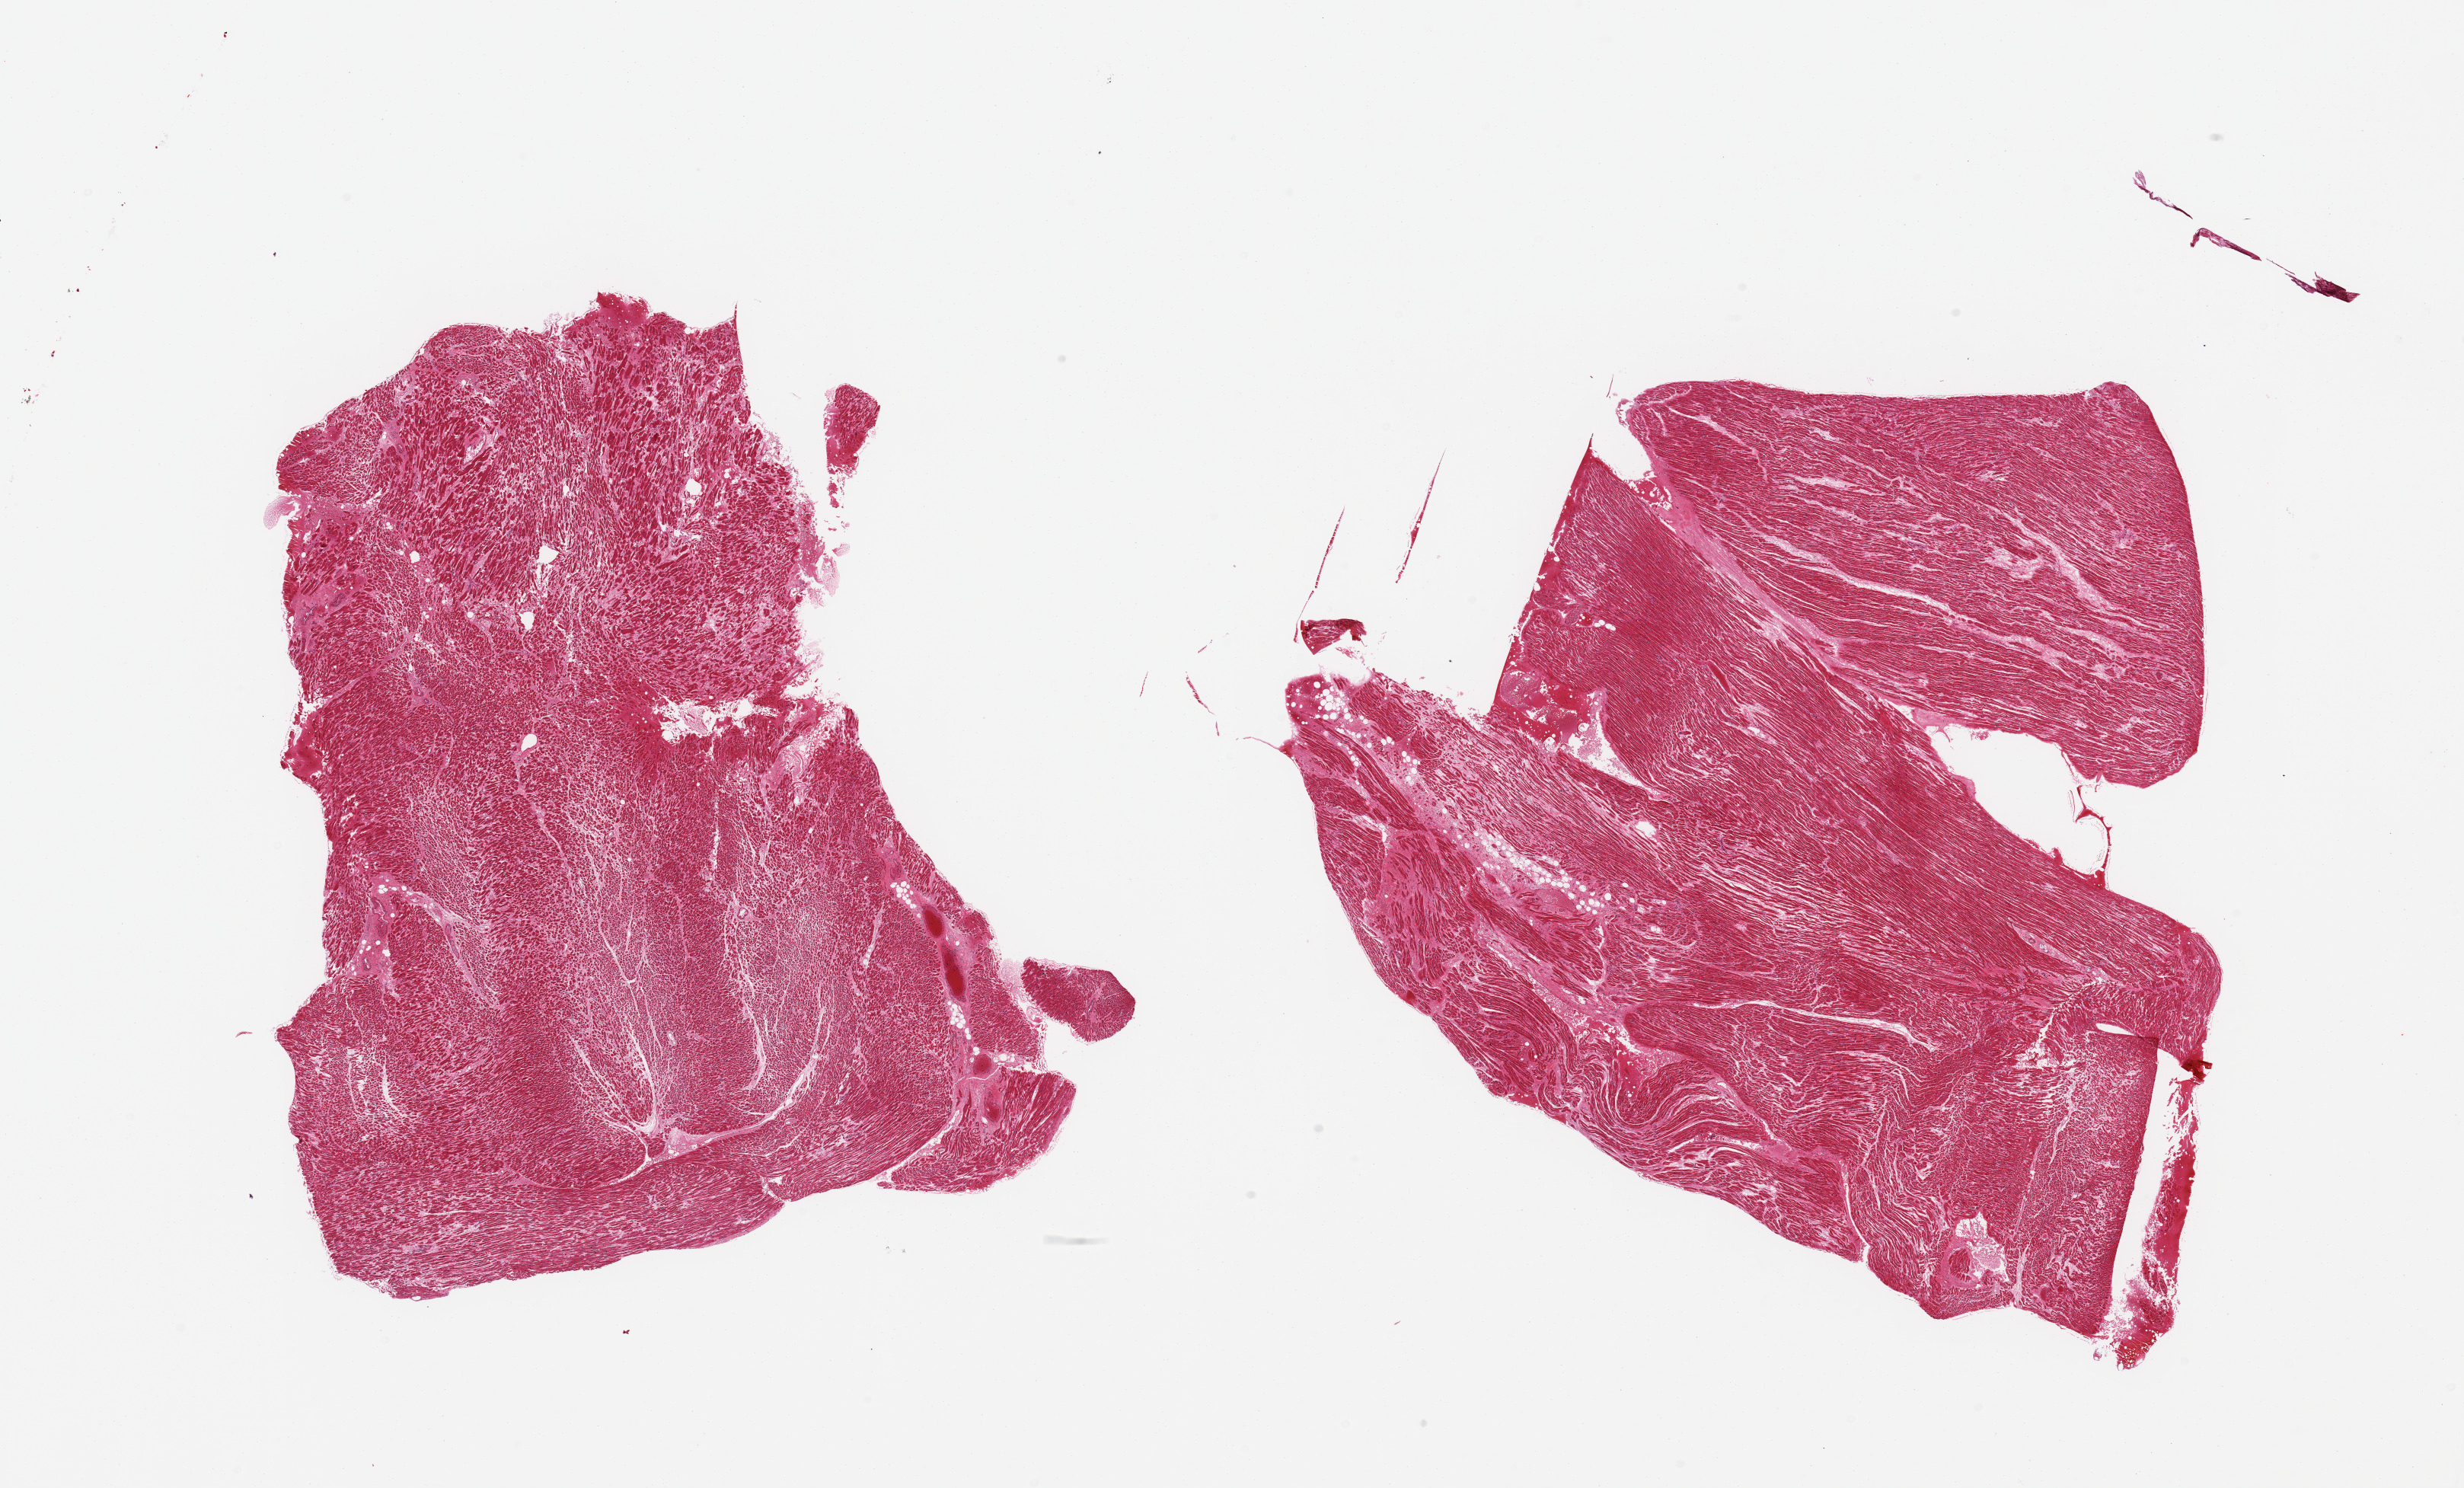
Digitized H&E-stained section, whole scanned area (about 25.6 x 15.5 mm, slide scanned at 20x) shown as a low-resolution overview; PAXgene-fixed, paraffin-embedded tissue; section of heart (target tissue); tissue donor sample. Male donor.
* pathologist's review note for this sample: 2 pieces, severe diffuse chronic ischemic damage